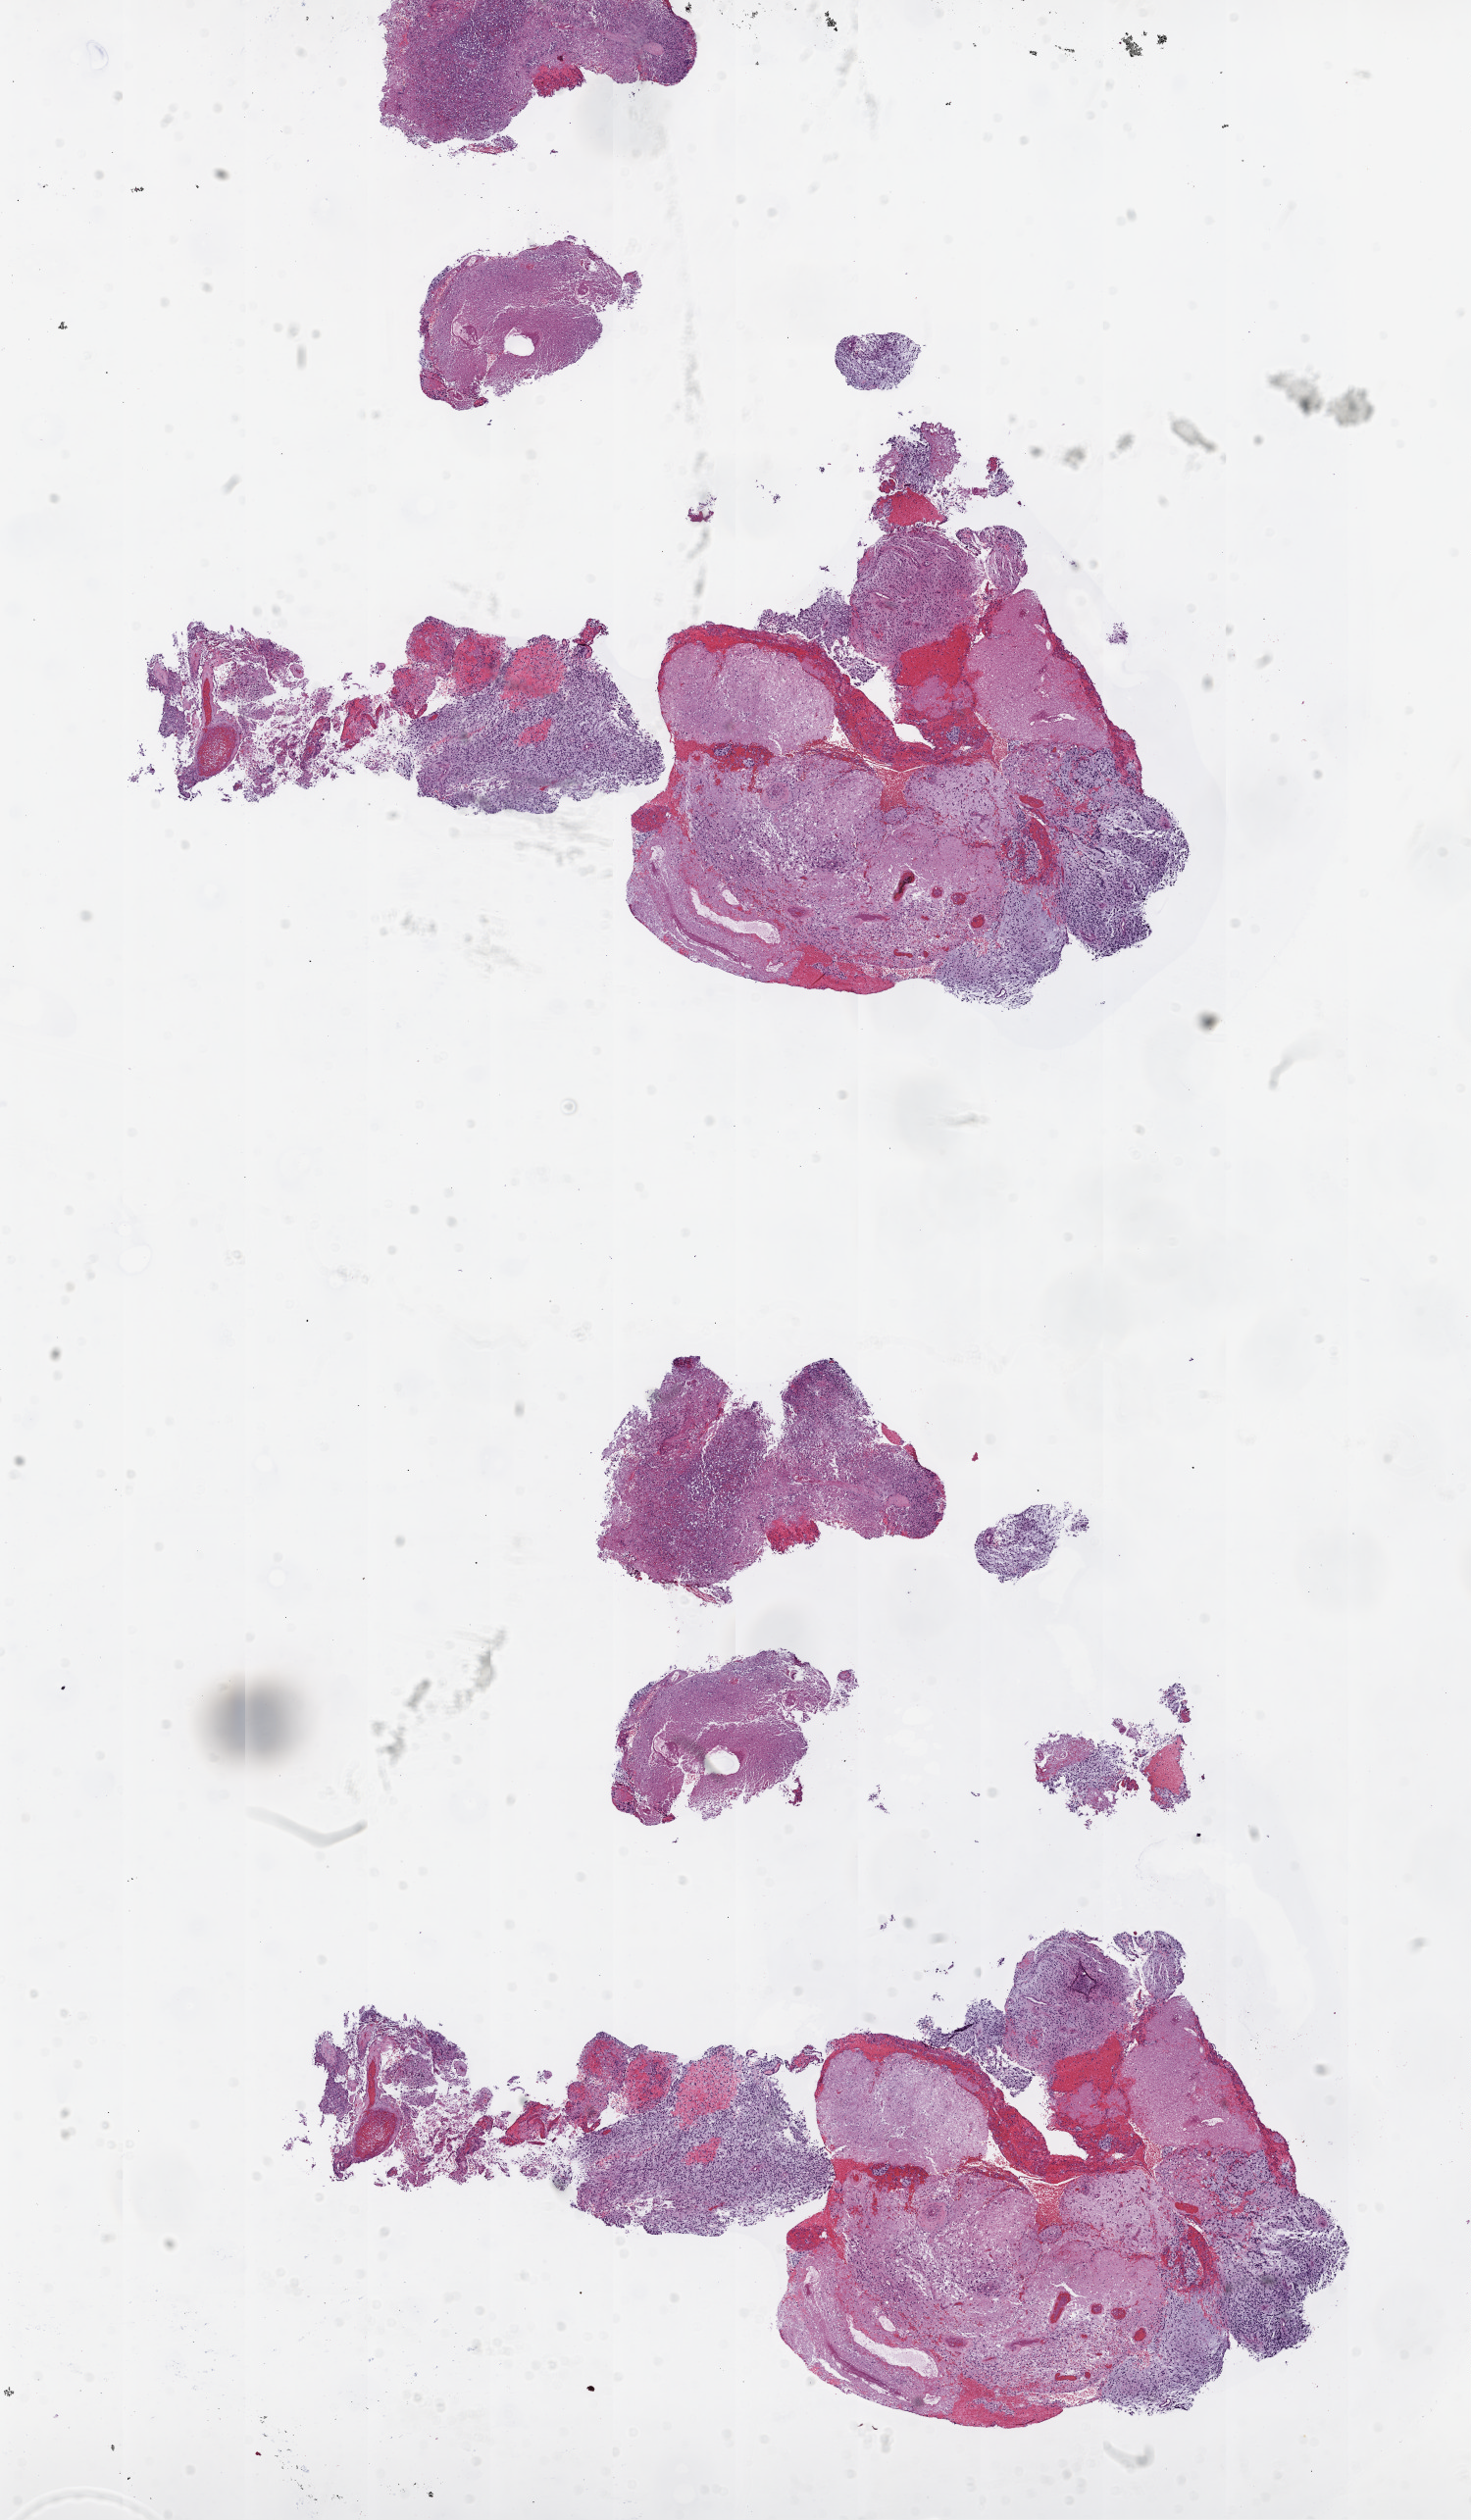
Whole-slide histology image, H&E-stained, shown as a low-resolution overview of the whole scanned area (about 12.0 x 20.6 mm), frozen section, sample: primary tumour, brain. Female patient; age at initial diagnosis 81 years. Slide review estimates, as recorded: tumour cells 80%, tumour nuclei 80%, normal cells 0%, stromal cells 2%, necrosis 20%.
• histologic diagnosis: Glioblastoma